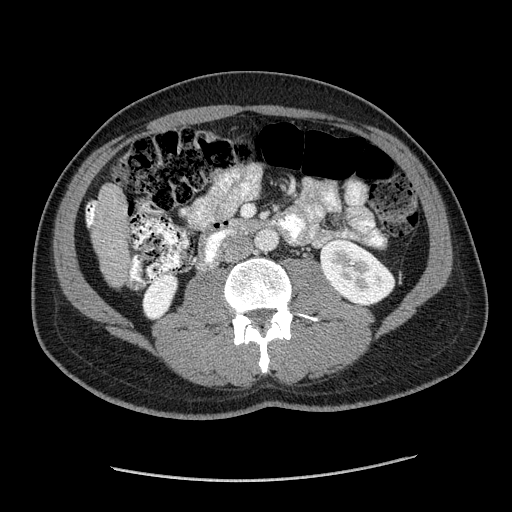
Contrast-enhanced abdominal CT (liver protocol), one axial slice; position 35 of 182 along the scan axis; reconstruction kernel STANDARD; 120 kVp; soft-tissue window (W 400 / L 40 HU); 2.5 mm slice thickness; 512 × 512 image matrix, field of view 400 × 400 mm. Case-level facts recorded for this patient, not image findings: diagnosis: hepatocellular carcinoma (patient treated with transarterial chemoembolisation; whether this scan precedes or follows treatment is not stated here); TNM stage (as recorded): Stage-I; Child-Pugh class: A; tumour differentiation: well differentiated; tumour nodularity: uninodular.
Structures marked on this image (semi-automatically segmented with operator editing):
- liver parenchyma outside the tumour (the mass and vessels are separate outlines, so this box may not span the whole liver): bounding box (x1, y1, x2, y2) in pixels: (86, 183, 130, 286)
- liver vessels: (87, 203, 95, 226)